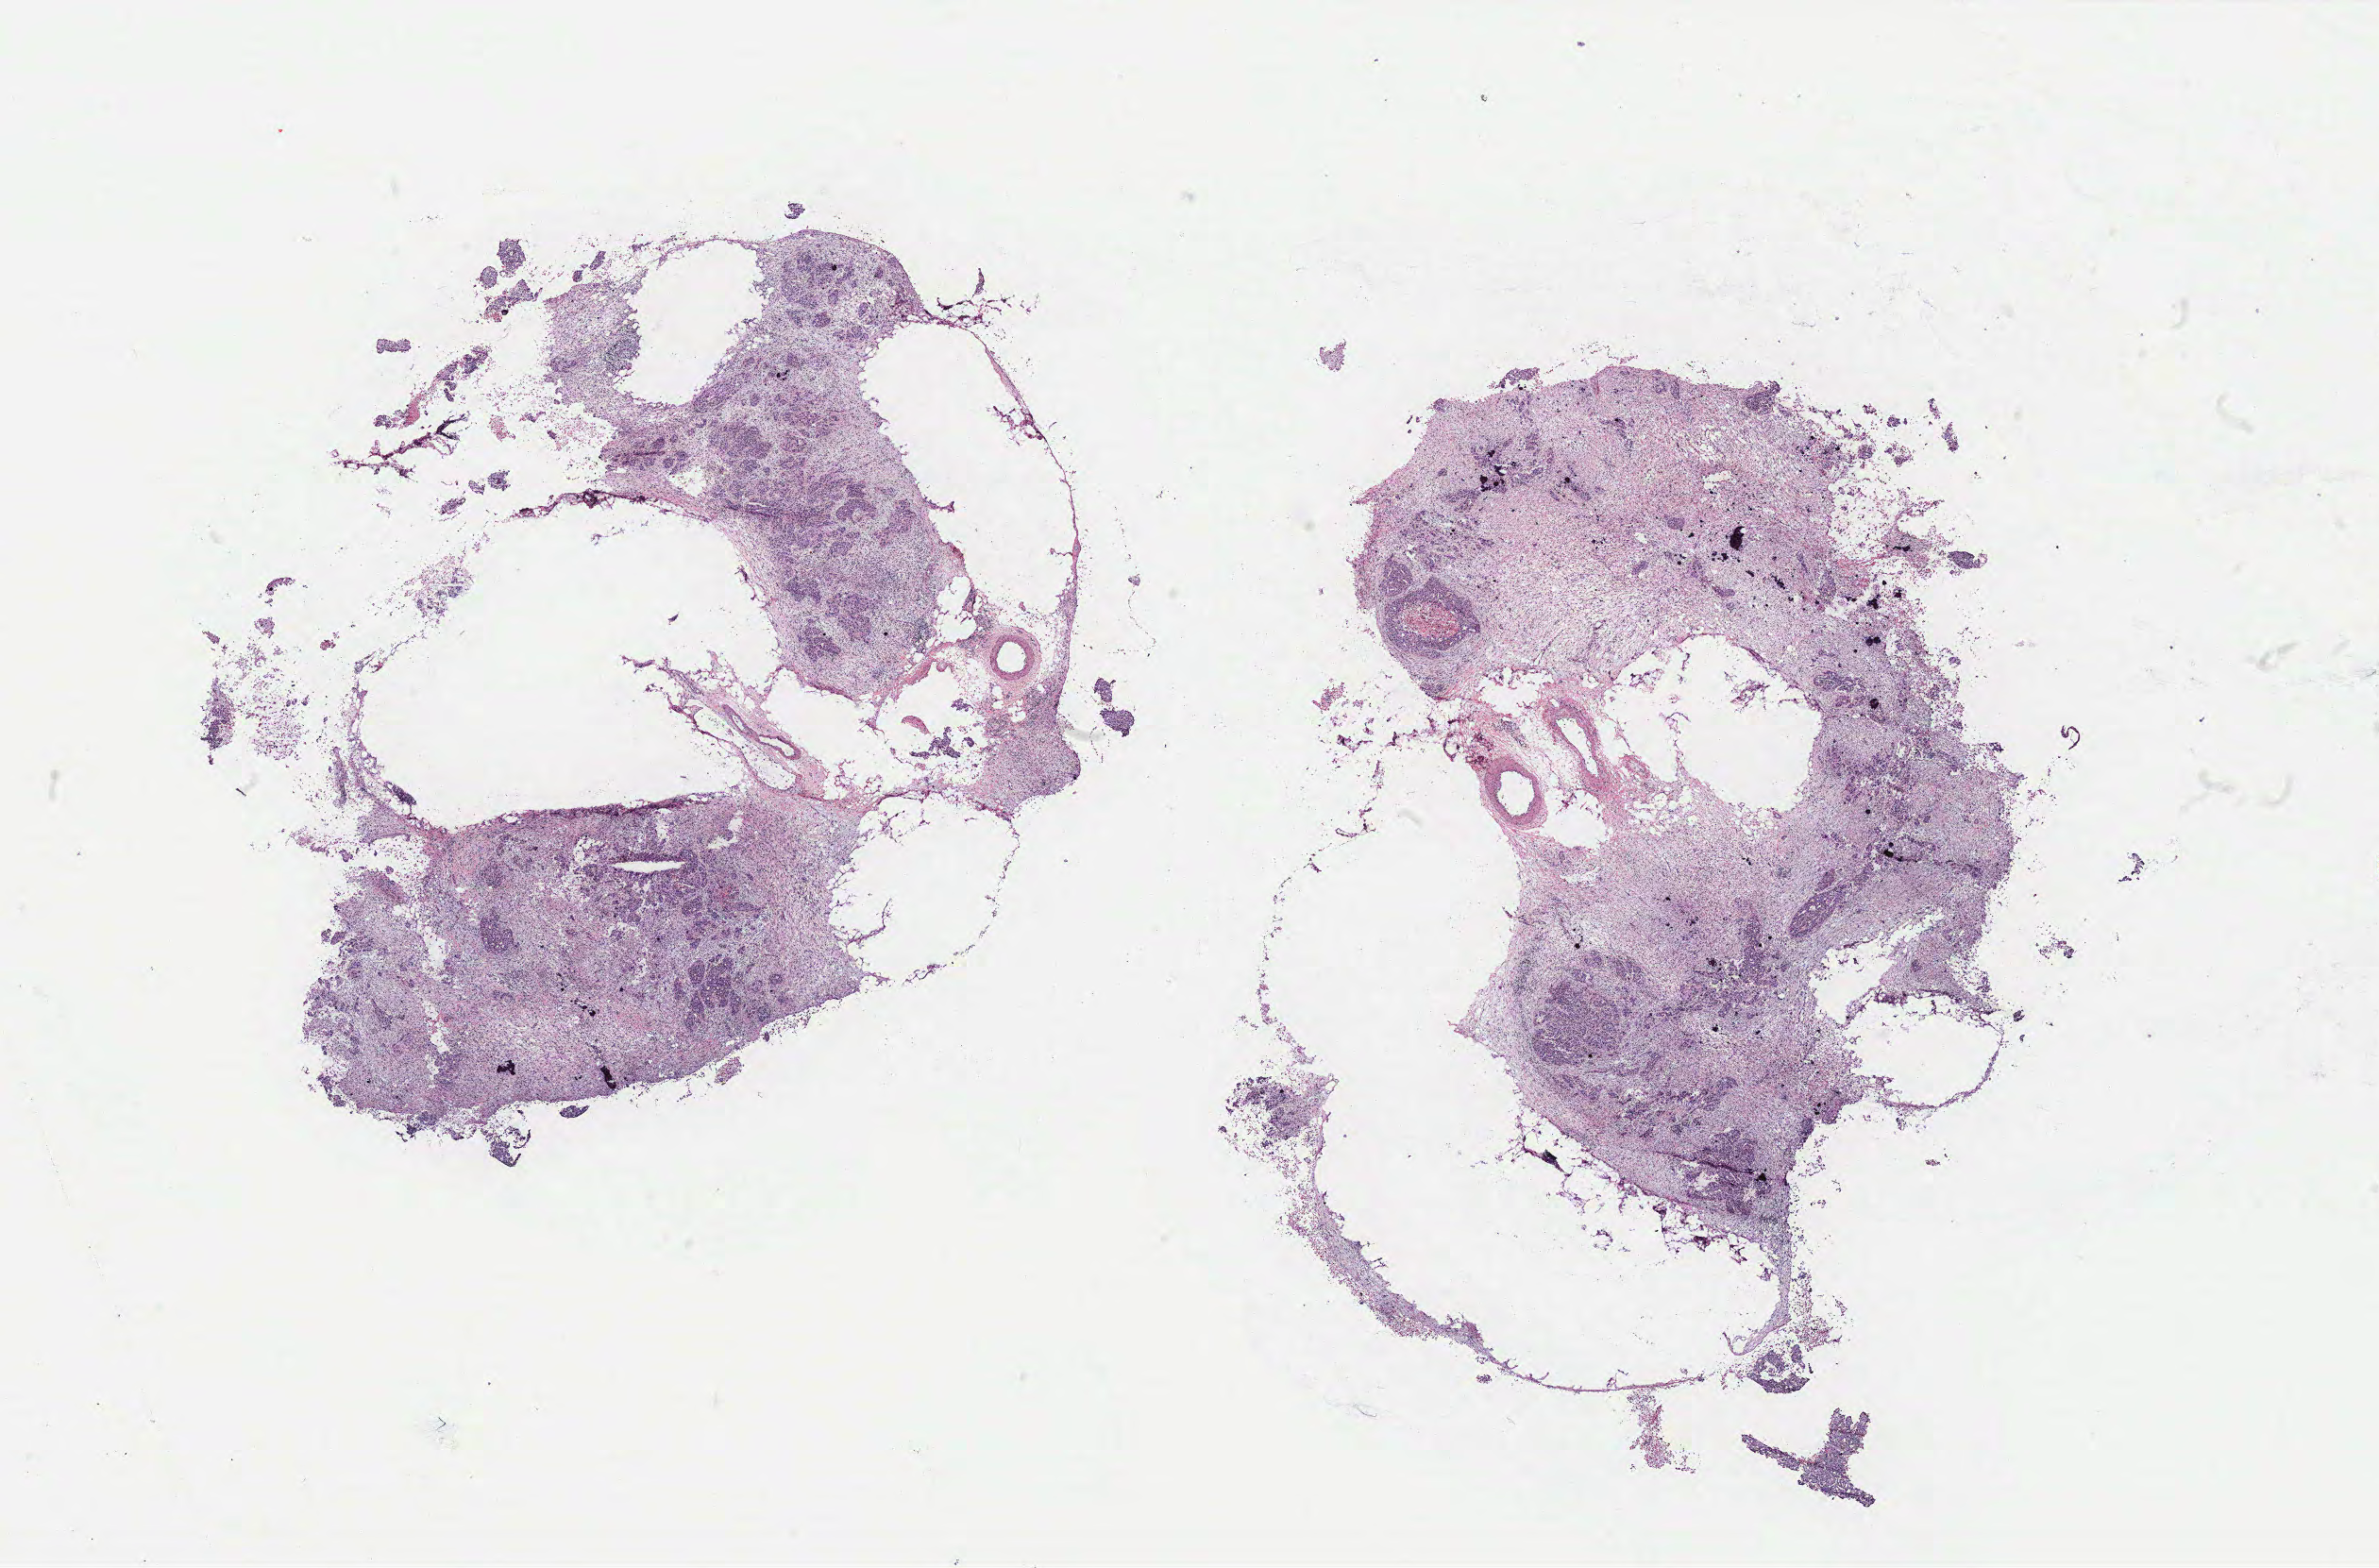
Whole-slide histology image, H&E, low-resolution overview of the scanned area, about 20.2 x 13.3 mm. Tumour tissue sample, ovary. Patient: female, age 53 years.
Primary tumour site (as recorded): fallopian tube. Histologic diagnosis: Serous adenocarcinoma, NOS (fallopian tube).